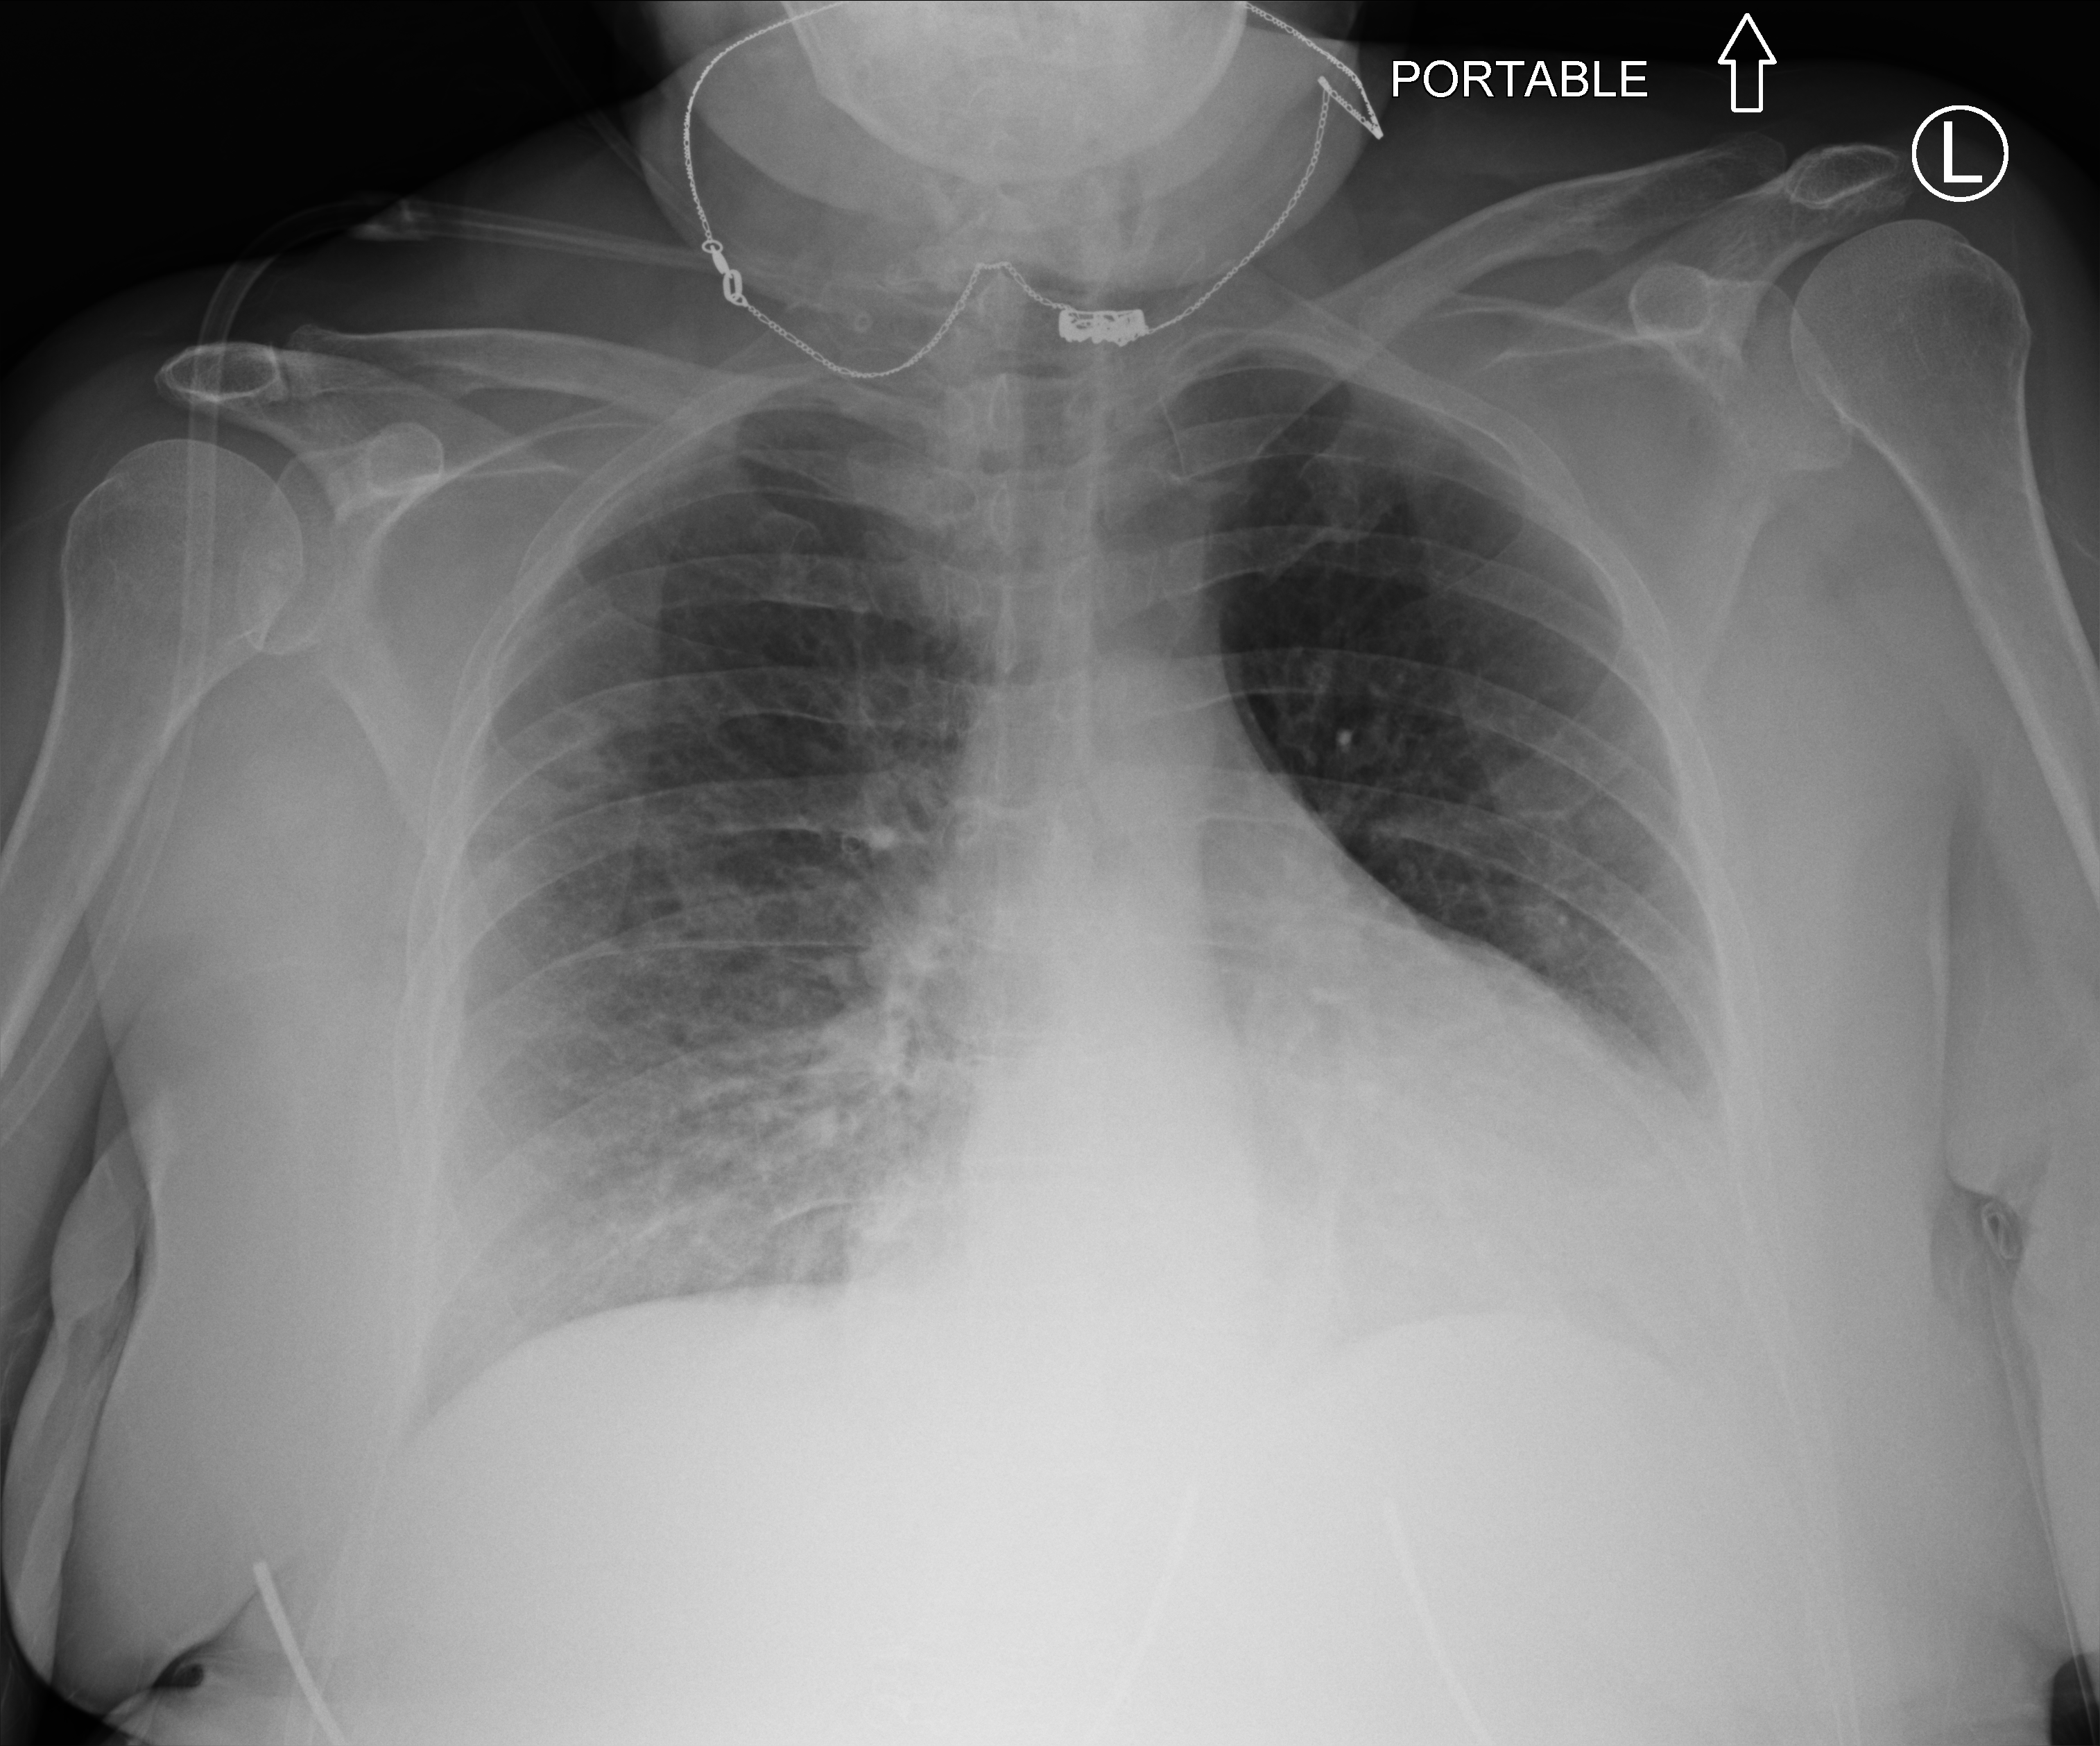
Chest X-ray (portable), anteroposterior (AP) projection. Patient hospitalised with COVID-19; female, aged 18–59 years.
Admission-level facts for this patient (not findings on this image; timing relative to this image not recorded):
- length of hospital stay: 2 days
- smoking status (admission record): never
- mechanically ventilated during this hospital stay: no